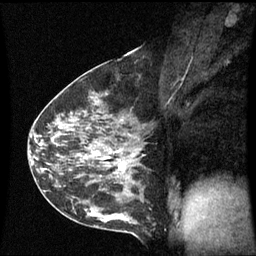
Breast MRI (dynamic contrast-enhanced), one sagittal slice. Slice 33 of 60 in the series (ordered by position). Dynamic contrast-enhanced series, image 2 of 3 at this slice position (ordered by acquisition). 1.5 T. TE 4.2 ms, TR 8.9 ms. 2.3 mm slice thickness. 256 × 256 image matrix. Patient: female, 43 years. From the clinical record (not read from this slice): setting: breast cancer imaged before/during neoadjuvant chemotherapy; receptor status: HER2-positive.
Structures marked on this image (semi-automatic segmentation, software-assisted and operator-edited):
- analysis volume of interest (the breast-tissue region the enhancement analysis was run in; not a lesion): bounding box [x1, y1, x2, y2] px = [56, 80, 145, 195]
- tumour enhancement mask (voxels above the 70 % enhancement threshold inside the analysis volume of interest): [98, 151, 127, 171]